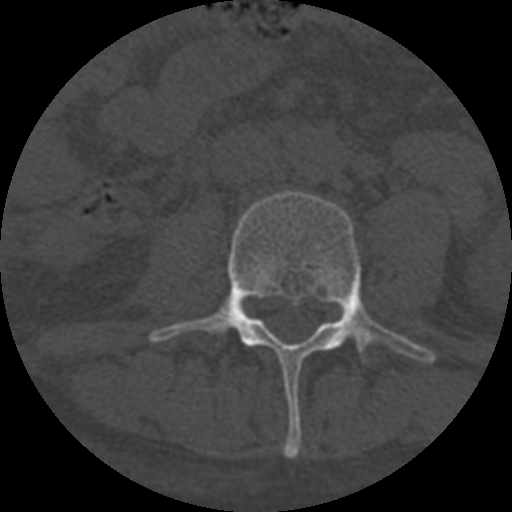
CT including the spine, one axial slice. Slice 233 of 708 in the series (ordered by position). Reconstruction kernel STANDARD. 120 kVp. One of 3 acquisitions stored at this slice position. Bone window (W 1800 / L 400 HU). 1.25 mm slice thickness. 512 × 512 image matrix, field of view 160 × 160 mm. Patient age 55 years. From the clinical record (not read from this slice): primary cancer: colon; vertebrae with lytic lesions (as recorded): T12, L1, L5.
Annotated regions visible in this slice (semi-automatically segmented with operator editing):
- L3 vertebra: bounding box [x1, y1, x2, y2] px = [149, 191, 436, 458]